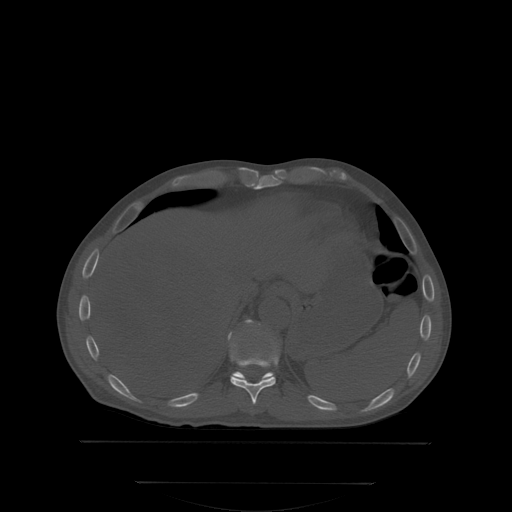
CT including the spine, one axial slice. Position 190 of 350 along the scan axis. Bone window (W 1800 / L 400 HU). 512 × 512 image matrix, field of view 500 × 500 mm. Patient: male, 58 years. From the clinical record (not read from this slice): primary cancer: prostate; vertebrae with lytic lesions (as recorded): L1.
Structures marked on this image (semi-automatically segmented with operator editing):
- T10 vertebra: bounding box <231,356,277,405> (left, top, right, bottom; pixels)
- T11 vertebra: <234,371,271,380>